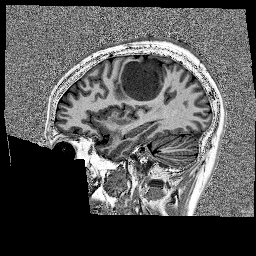
Brain MRI from a brain-tumour surgery series, one sagittal slice. Slice 56 of 176 in the series (ordered by position). 1 mm slice thickness. 256 × 256 image matrix, field of view 256 × 256 mm. From the clinical record (not read from this slice): histopathology: Glioblastoma; WHO grade: 4; IDH mutation: no; tumour location: Left Frontal.
Outlined on this slice (outlined manually by an expert reader):
- tumour: box from (x=118, y=58) to (x=175, y=105) px